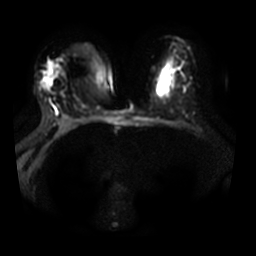
Breast MRI, one axial slice. Slice 18 of 31 in the series (ordered by position). Diffusion-weighted series; image 2 of 4 stored at this slice position (different b-values; order by instance number). 3 T. 5 mm slice thickness. 256 × 256 image matrix, field of view 350 × 350 mm. Female patient.
Outlined on this slice (expert manual segmentation):
- tumour on diffusion-weighted imaging: bounding box [x1, y1, x2, y2] px = [45, 61, 61, 87]